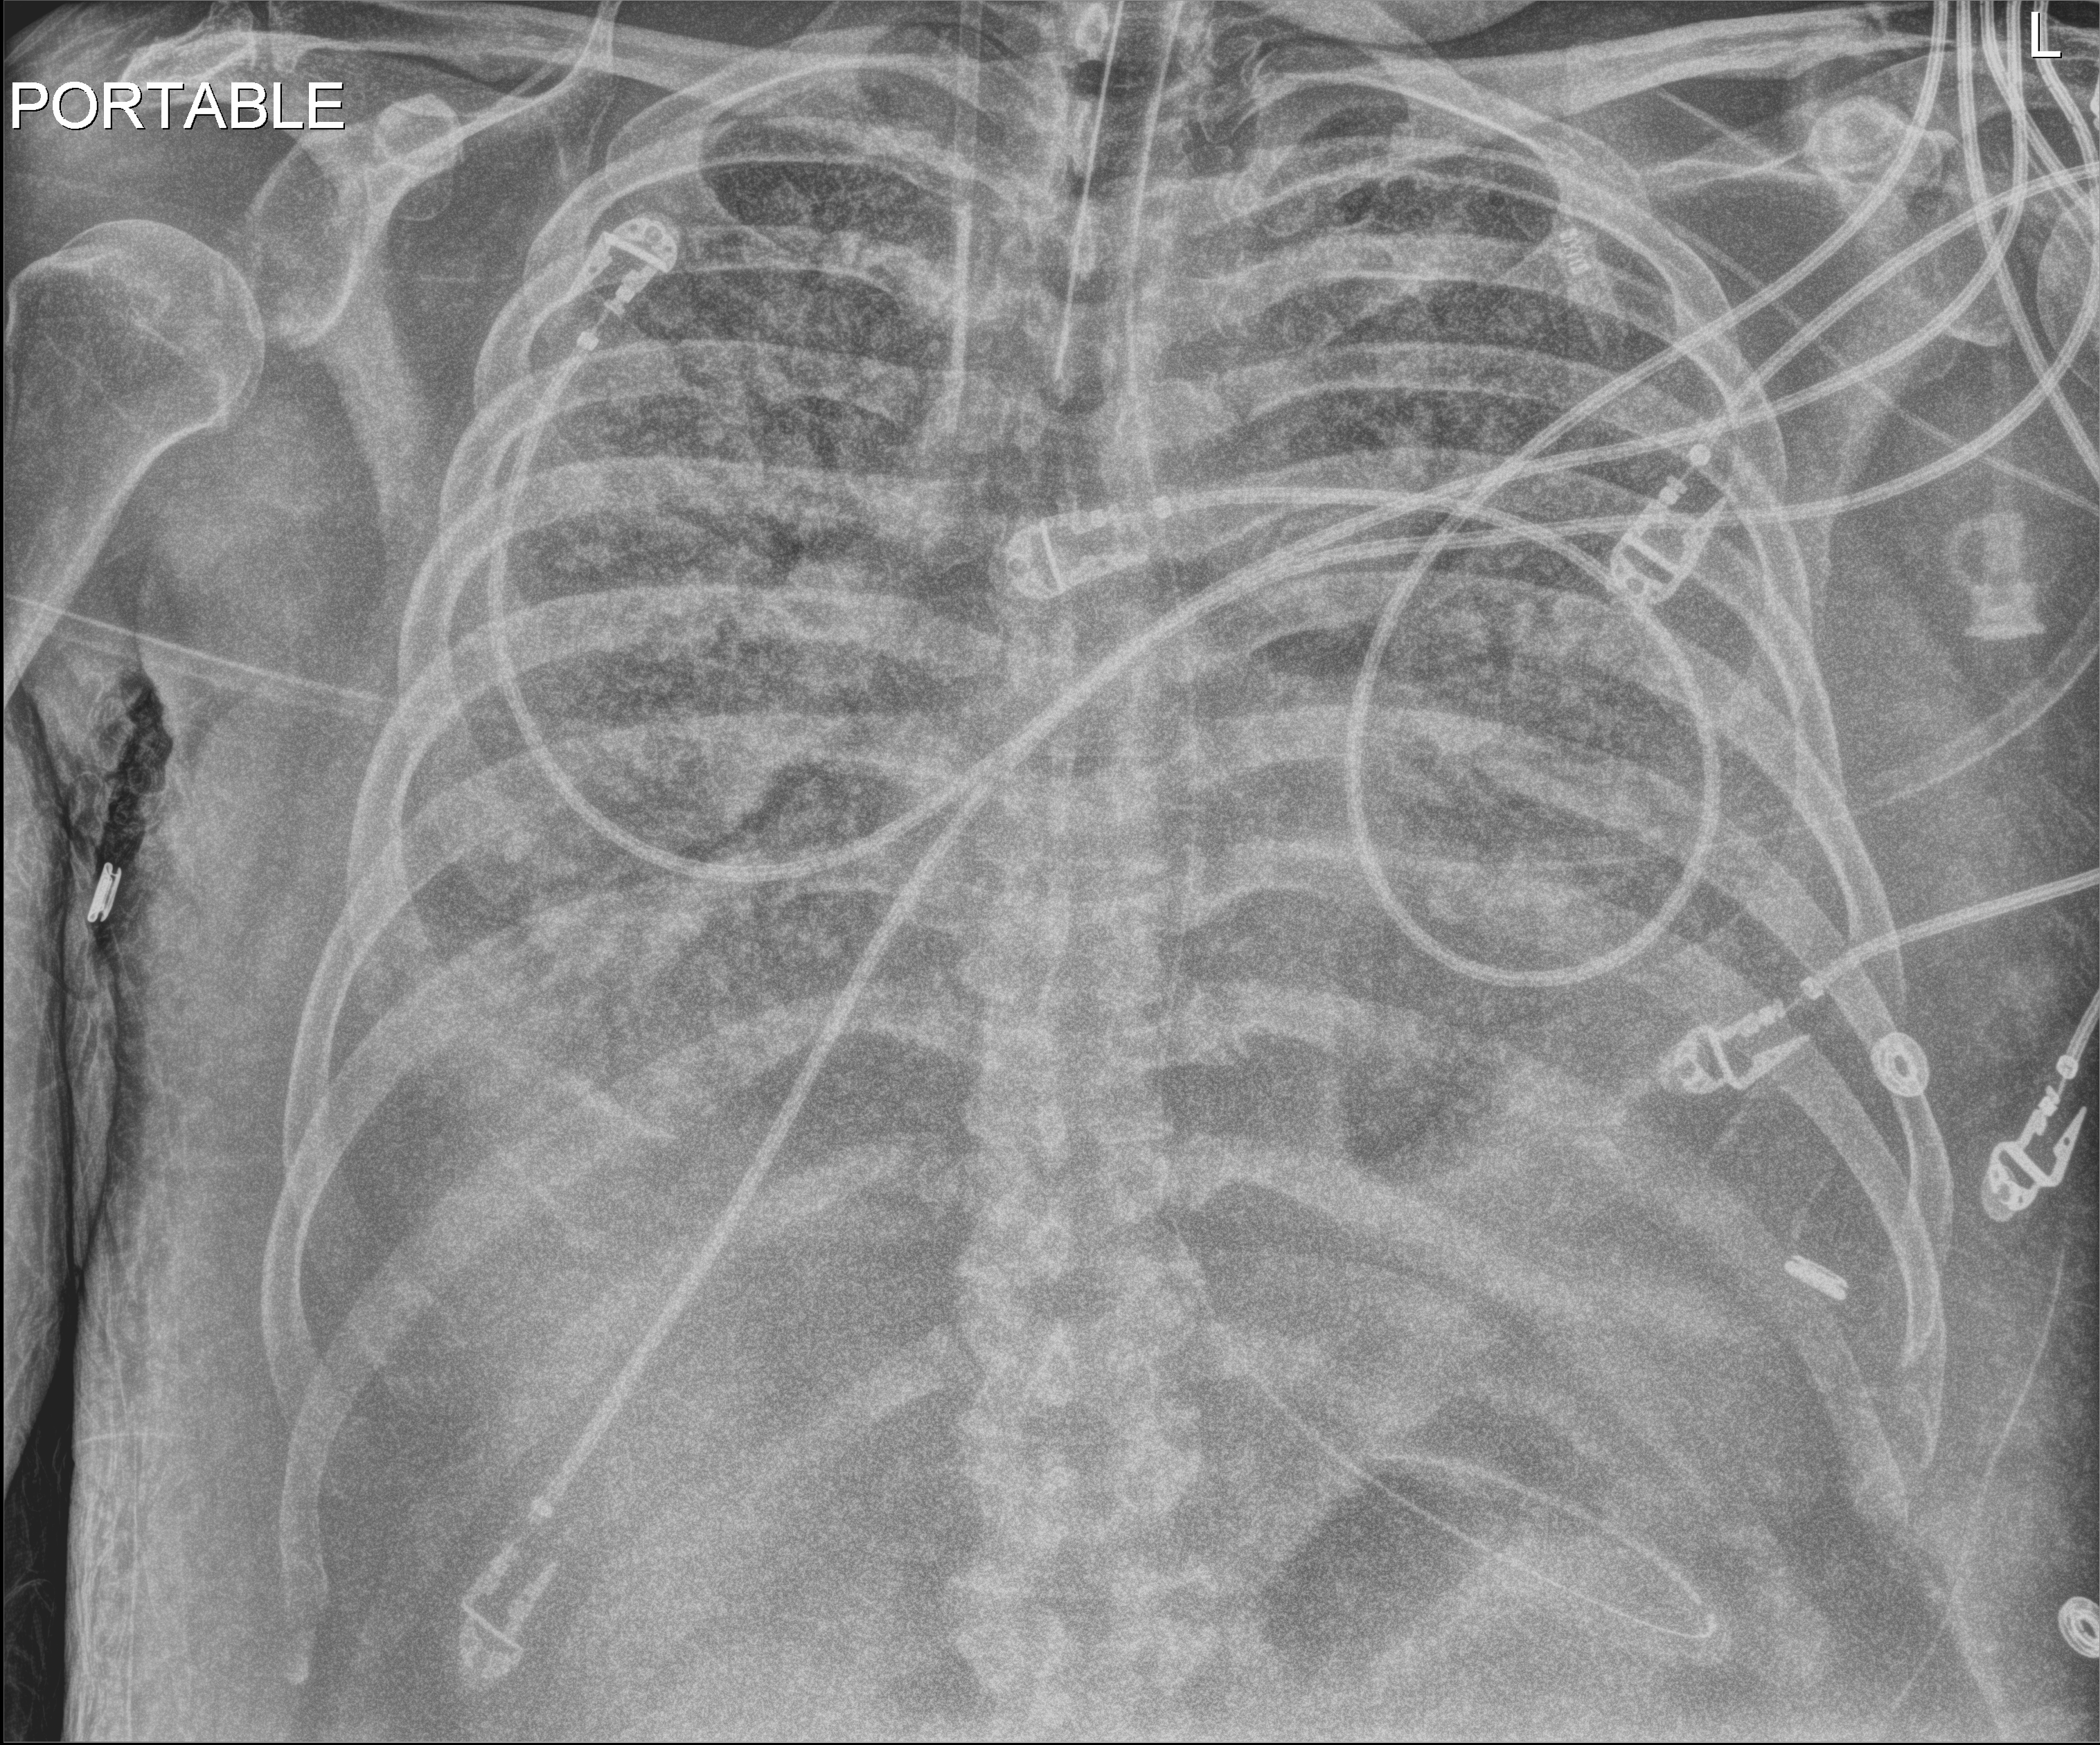
Portable chest radiograph; anteroposterior (AP) projection. Male patient hospitalised with COVID-19, age 60–74 years.
Hospital-stay facts (about this admission, not read from this image; timing relative to this image not recorded): mechanically ventilated during this hospital stay: yes; smoking status (admission record): never; chronic kidney disease (admission record): no.